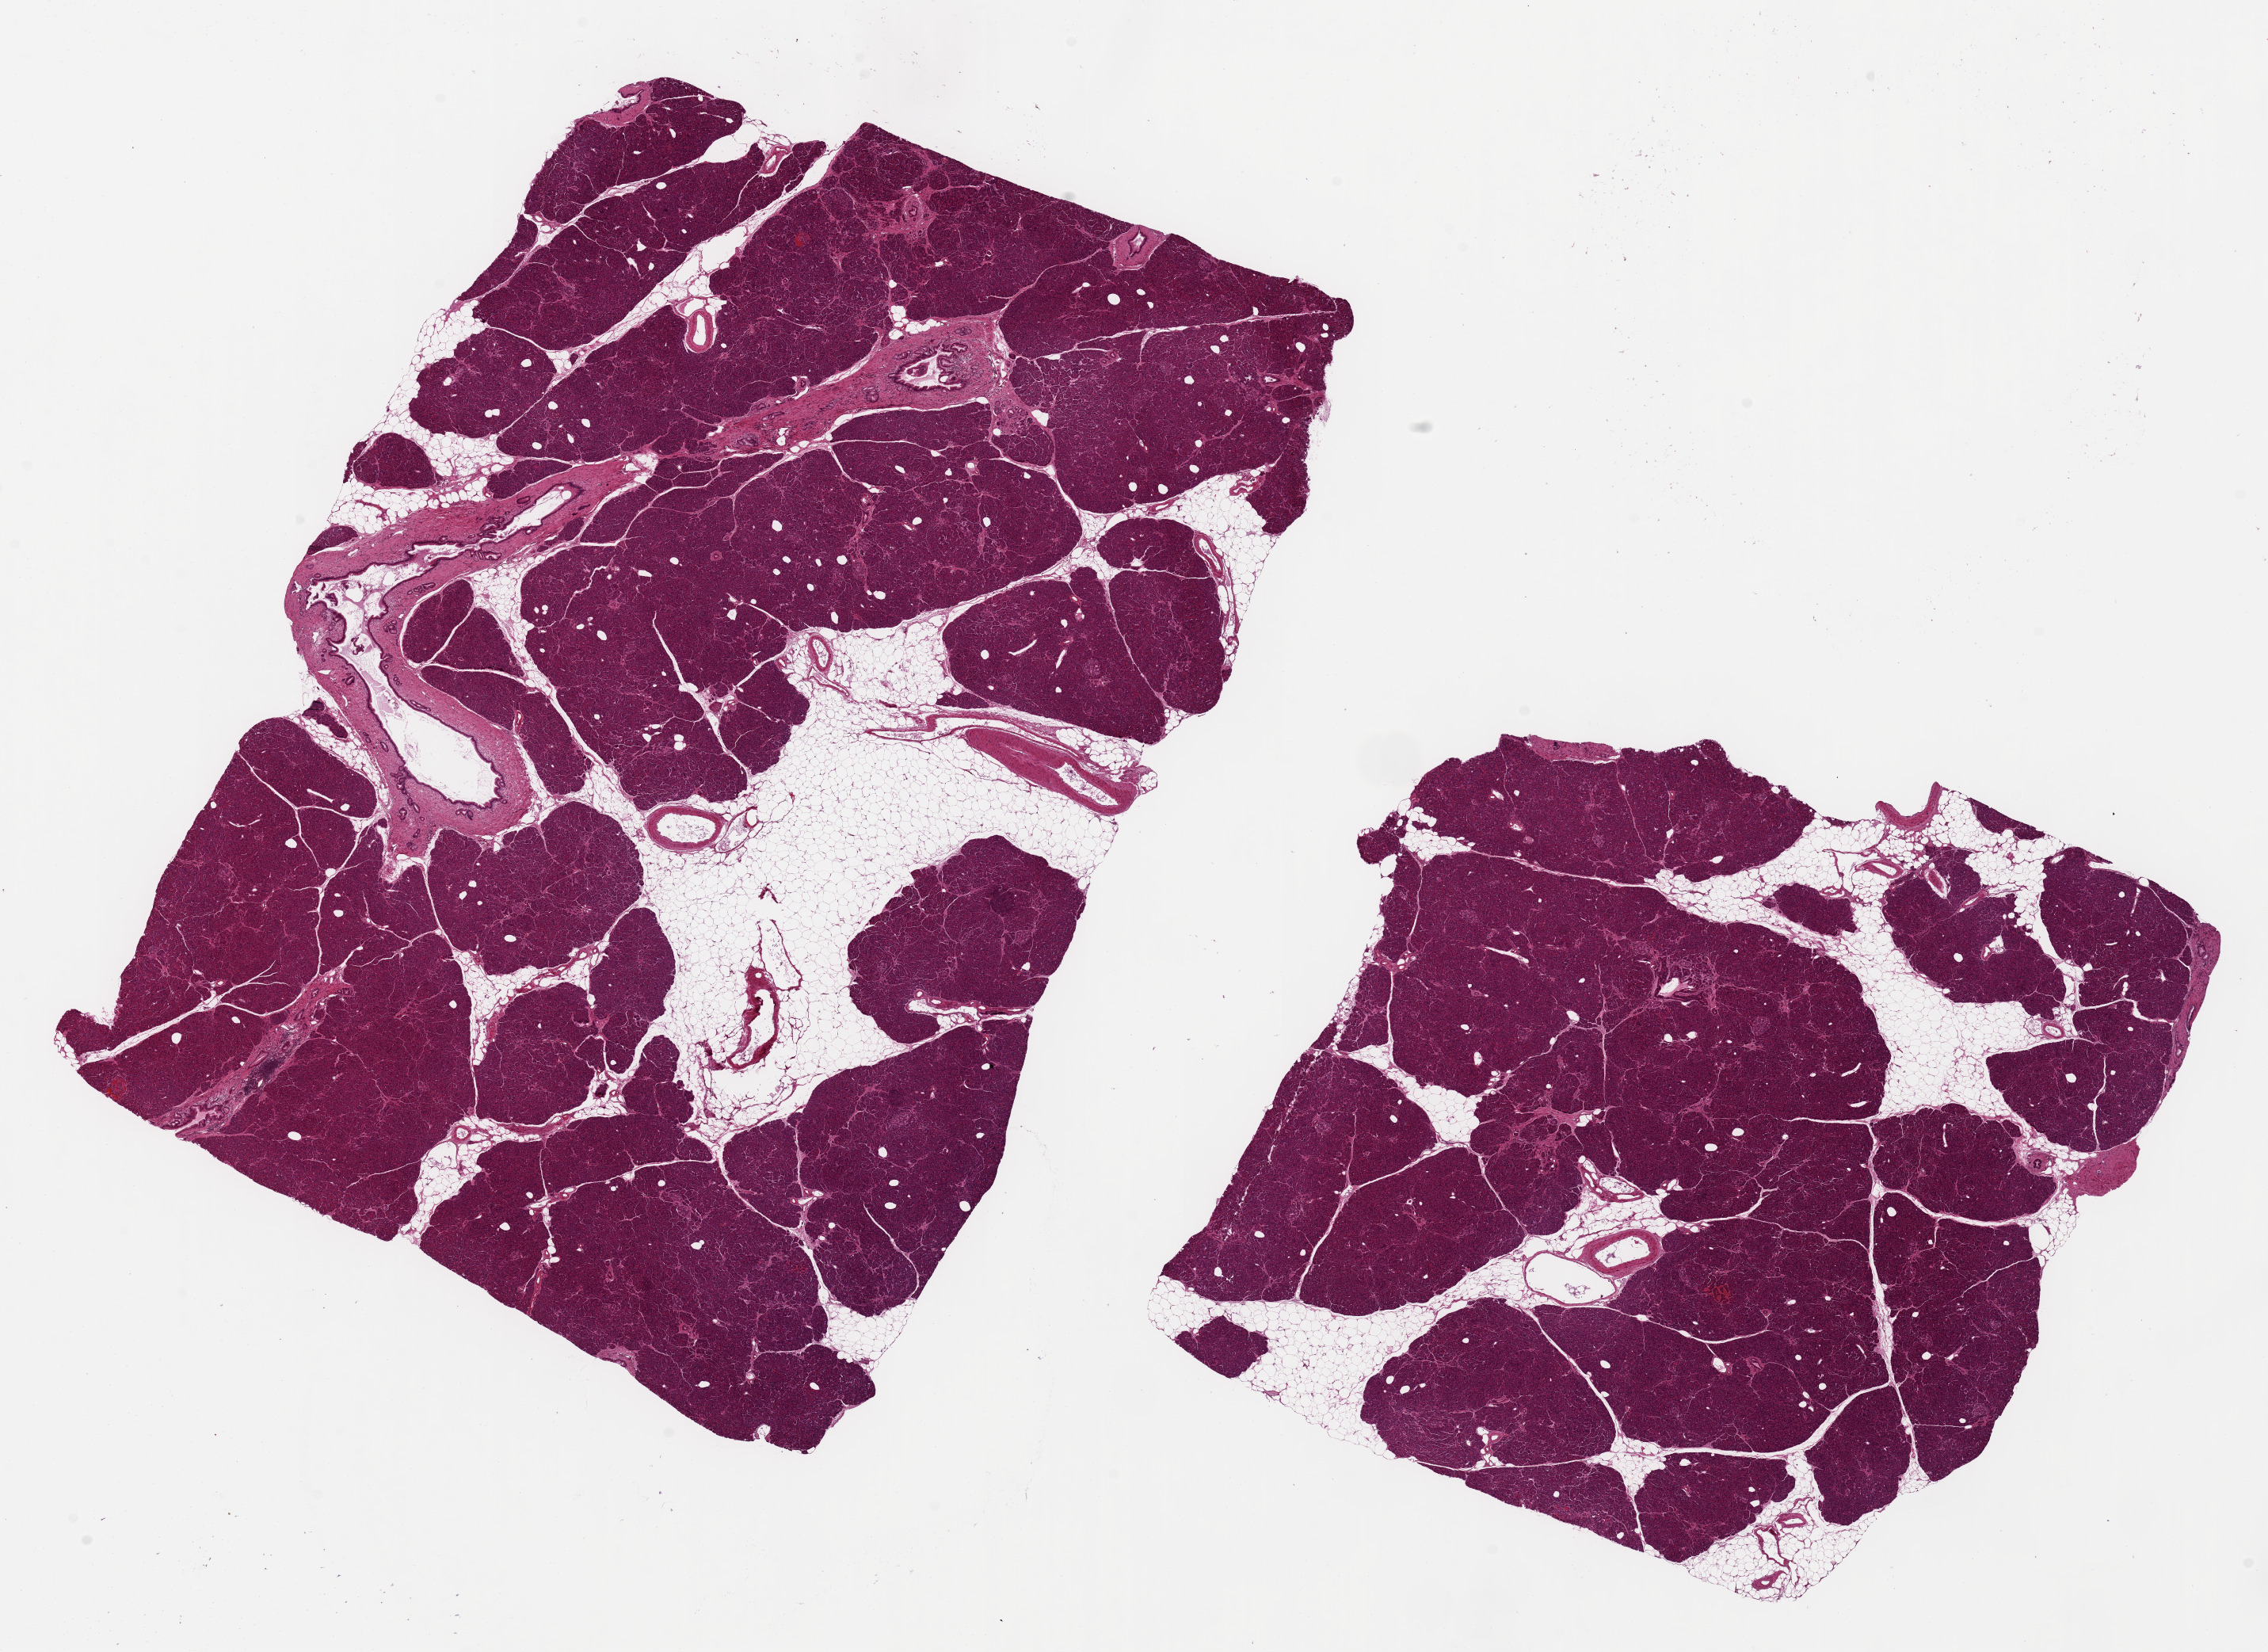
Haematoxylin and eosin whole-slide image, low-resolution overview of the scanned area, about 22.6 x 16.5 mm (from a 20x scan), PAXgene-fixed paraffin-embedded (PFPE) section, sampled site (target tissue): pancreas, tissue donor sample. Male donor.
• pathologist's review note for this sample: 2 pieces 12x8 & 7x7 mm; ~20% fat in each (included amongst the parenchyma, not outside)